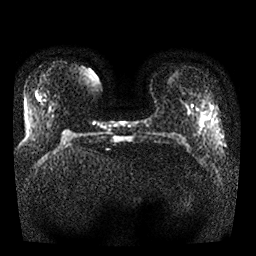
Breast MRI, one axial slice. Position 7 of 25 along the scan axis. Diffusion-weighted series; image 2 of 4 stored at this slice position (different b-values; order by instance number). 1.5 T. 4 mm slice thickness. 256 × 256 image matrix, field of view 340 × 340 mm. Female patient.
Annotated regions visible in this slice (manually delineated by an expert):
- tumour on diffusion-weighted imaging: bounding box [x1, y1, x2, y2] px = [200, 118, 205, 123]